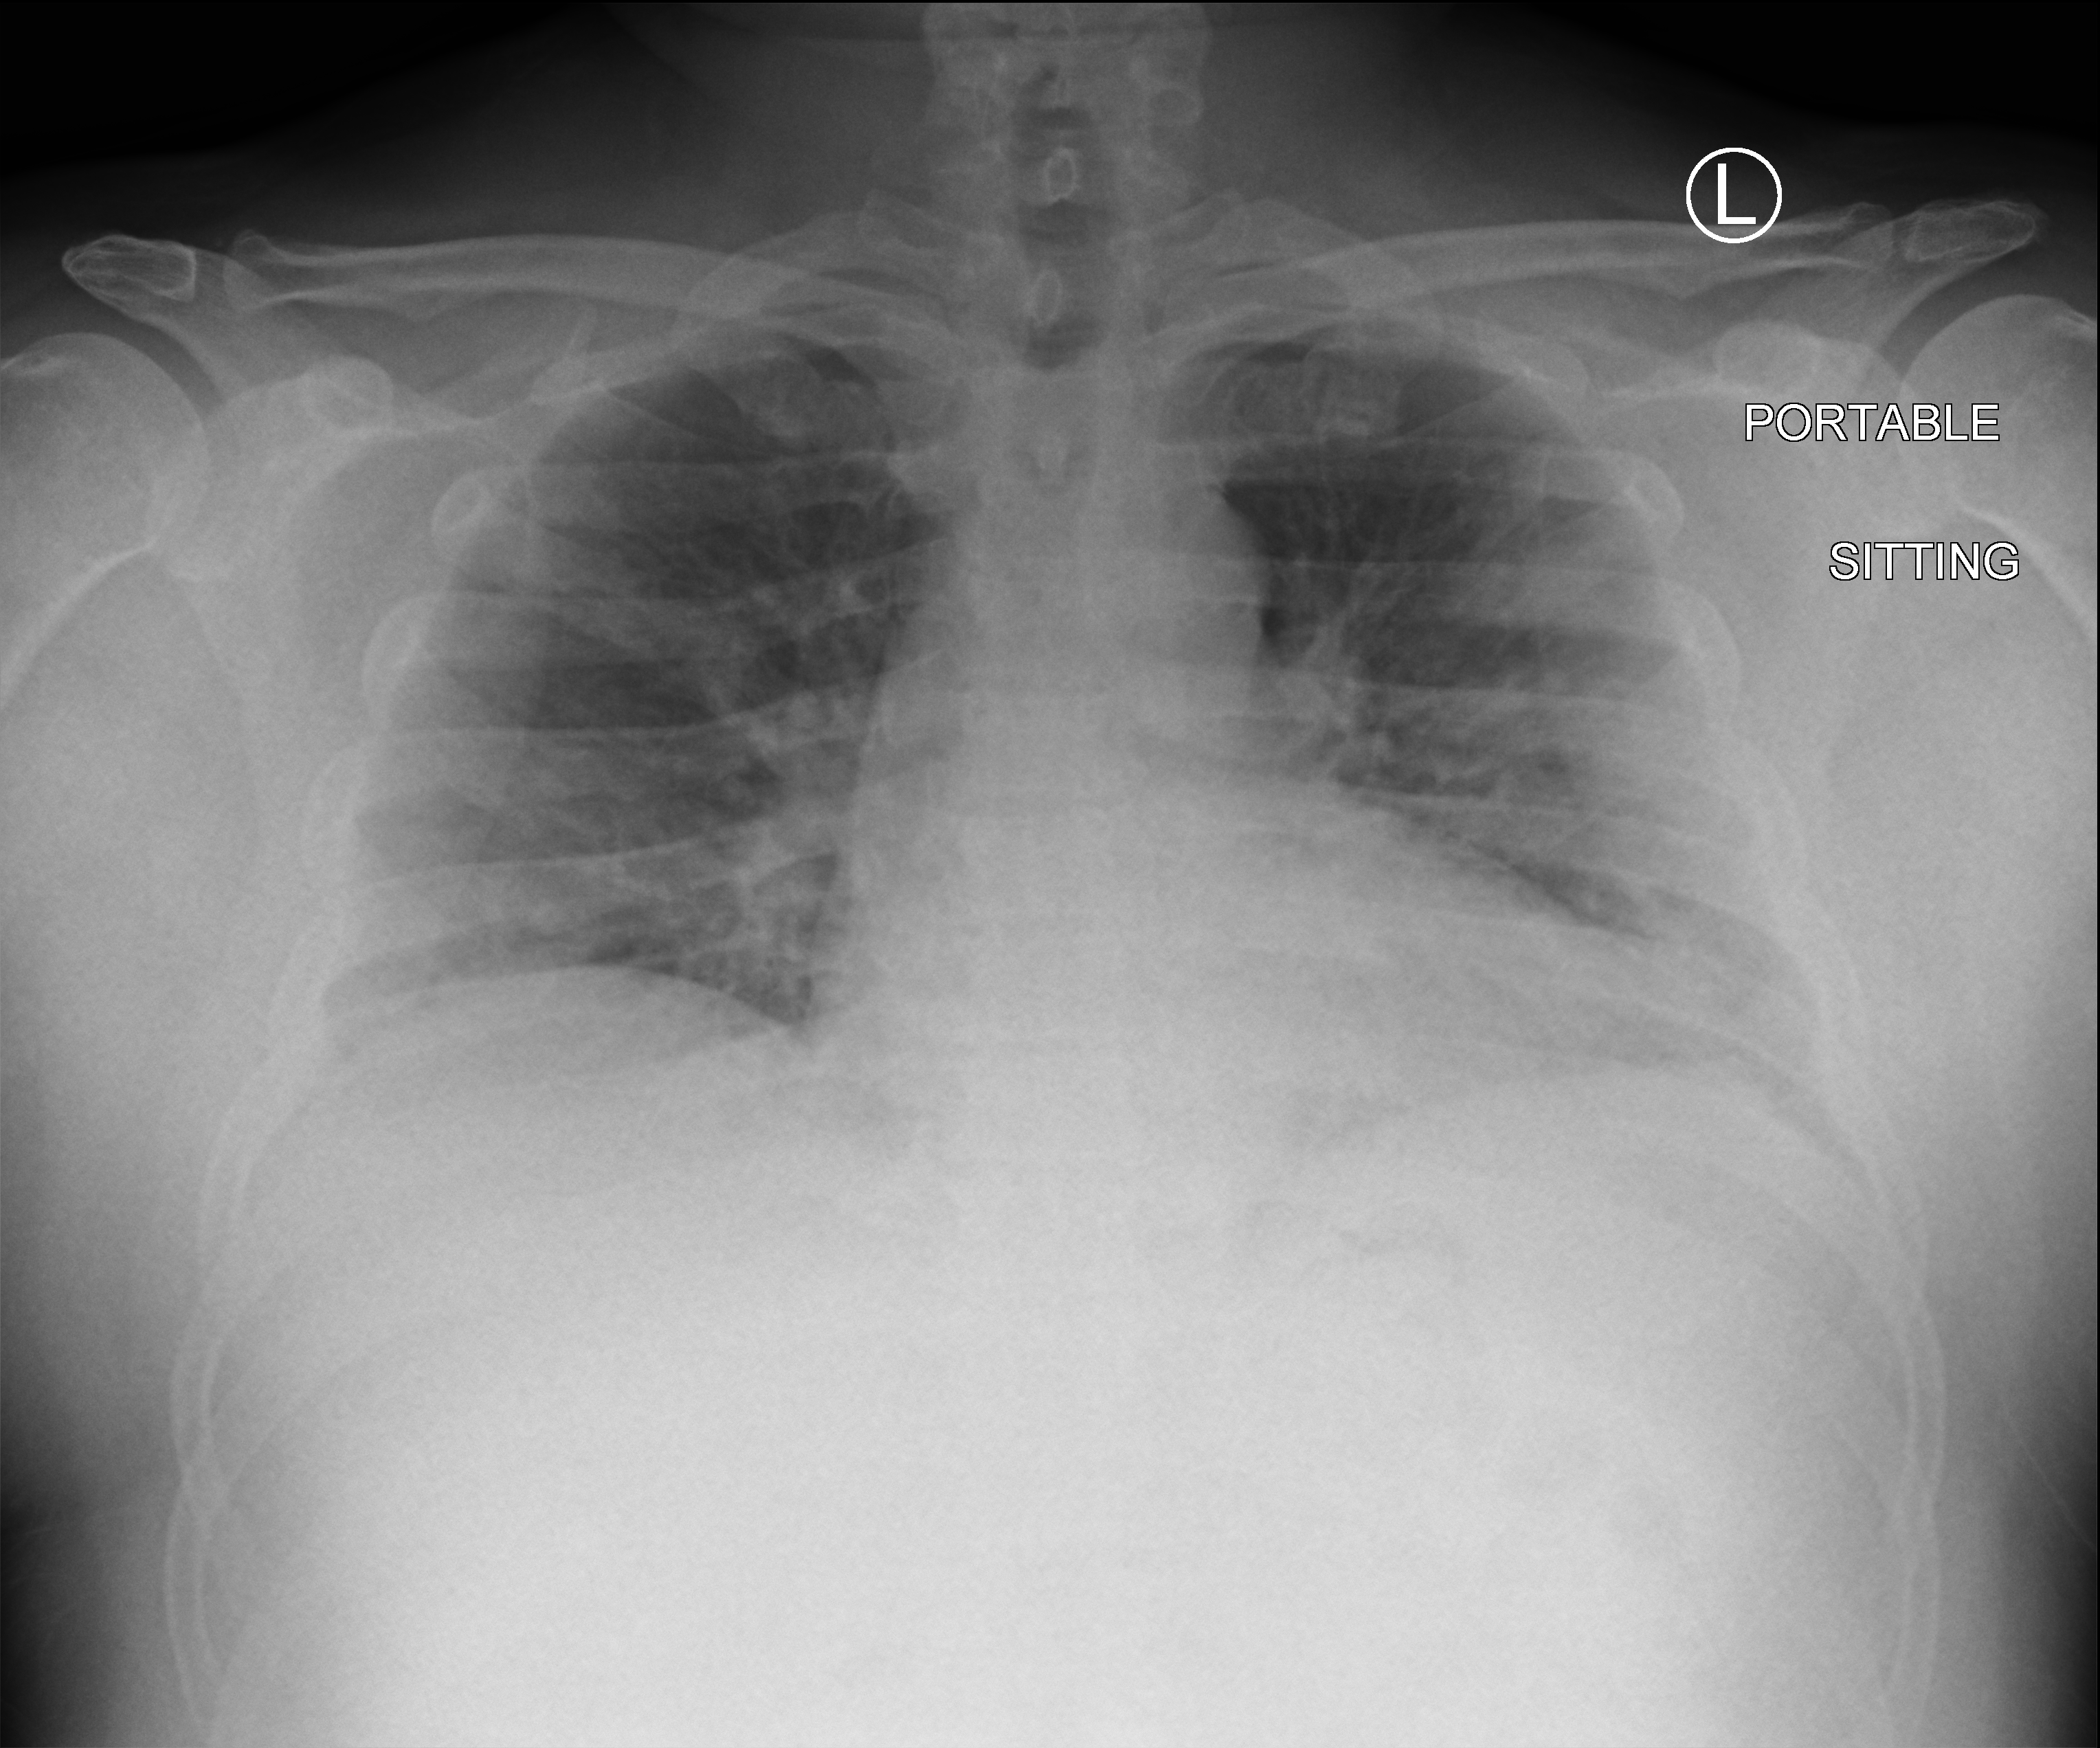
Chest X-ray (portable); anteroposterior (AP) projection. Male patient hospitalised with COVID-19, age 18–59 years.
Hospital-stay facts (about this admission, not read from this image; timing relative to this image not recorded):
- admitted to intensive care during this hospital stay: no